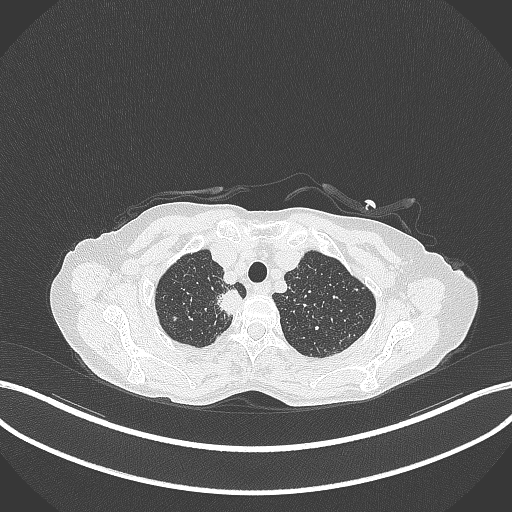
Chest CT, one axial slice; position 323 of 403 along the scan axis; reconstruction kernel B70f; 120 kVp; lung window (W 1500 / L -600 HU); 1 mm slice thickness; 512 × 512 image matrix, field of view 400 × 400 mm. Patient: female, 75 years. From the clinical record (not read from this slice): clinical TNM (as recorded): T1c N1 M1.
Outlined on this slice (bounding box drawn by a radiologist):
- lung tumour (recorded histology: adenocarcinoma): bounding box [x1, y1, x2, y2] px = [215, 286, 245, 318]